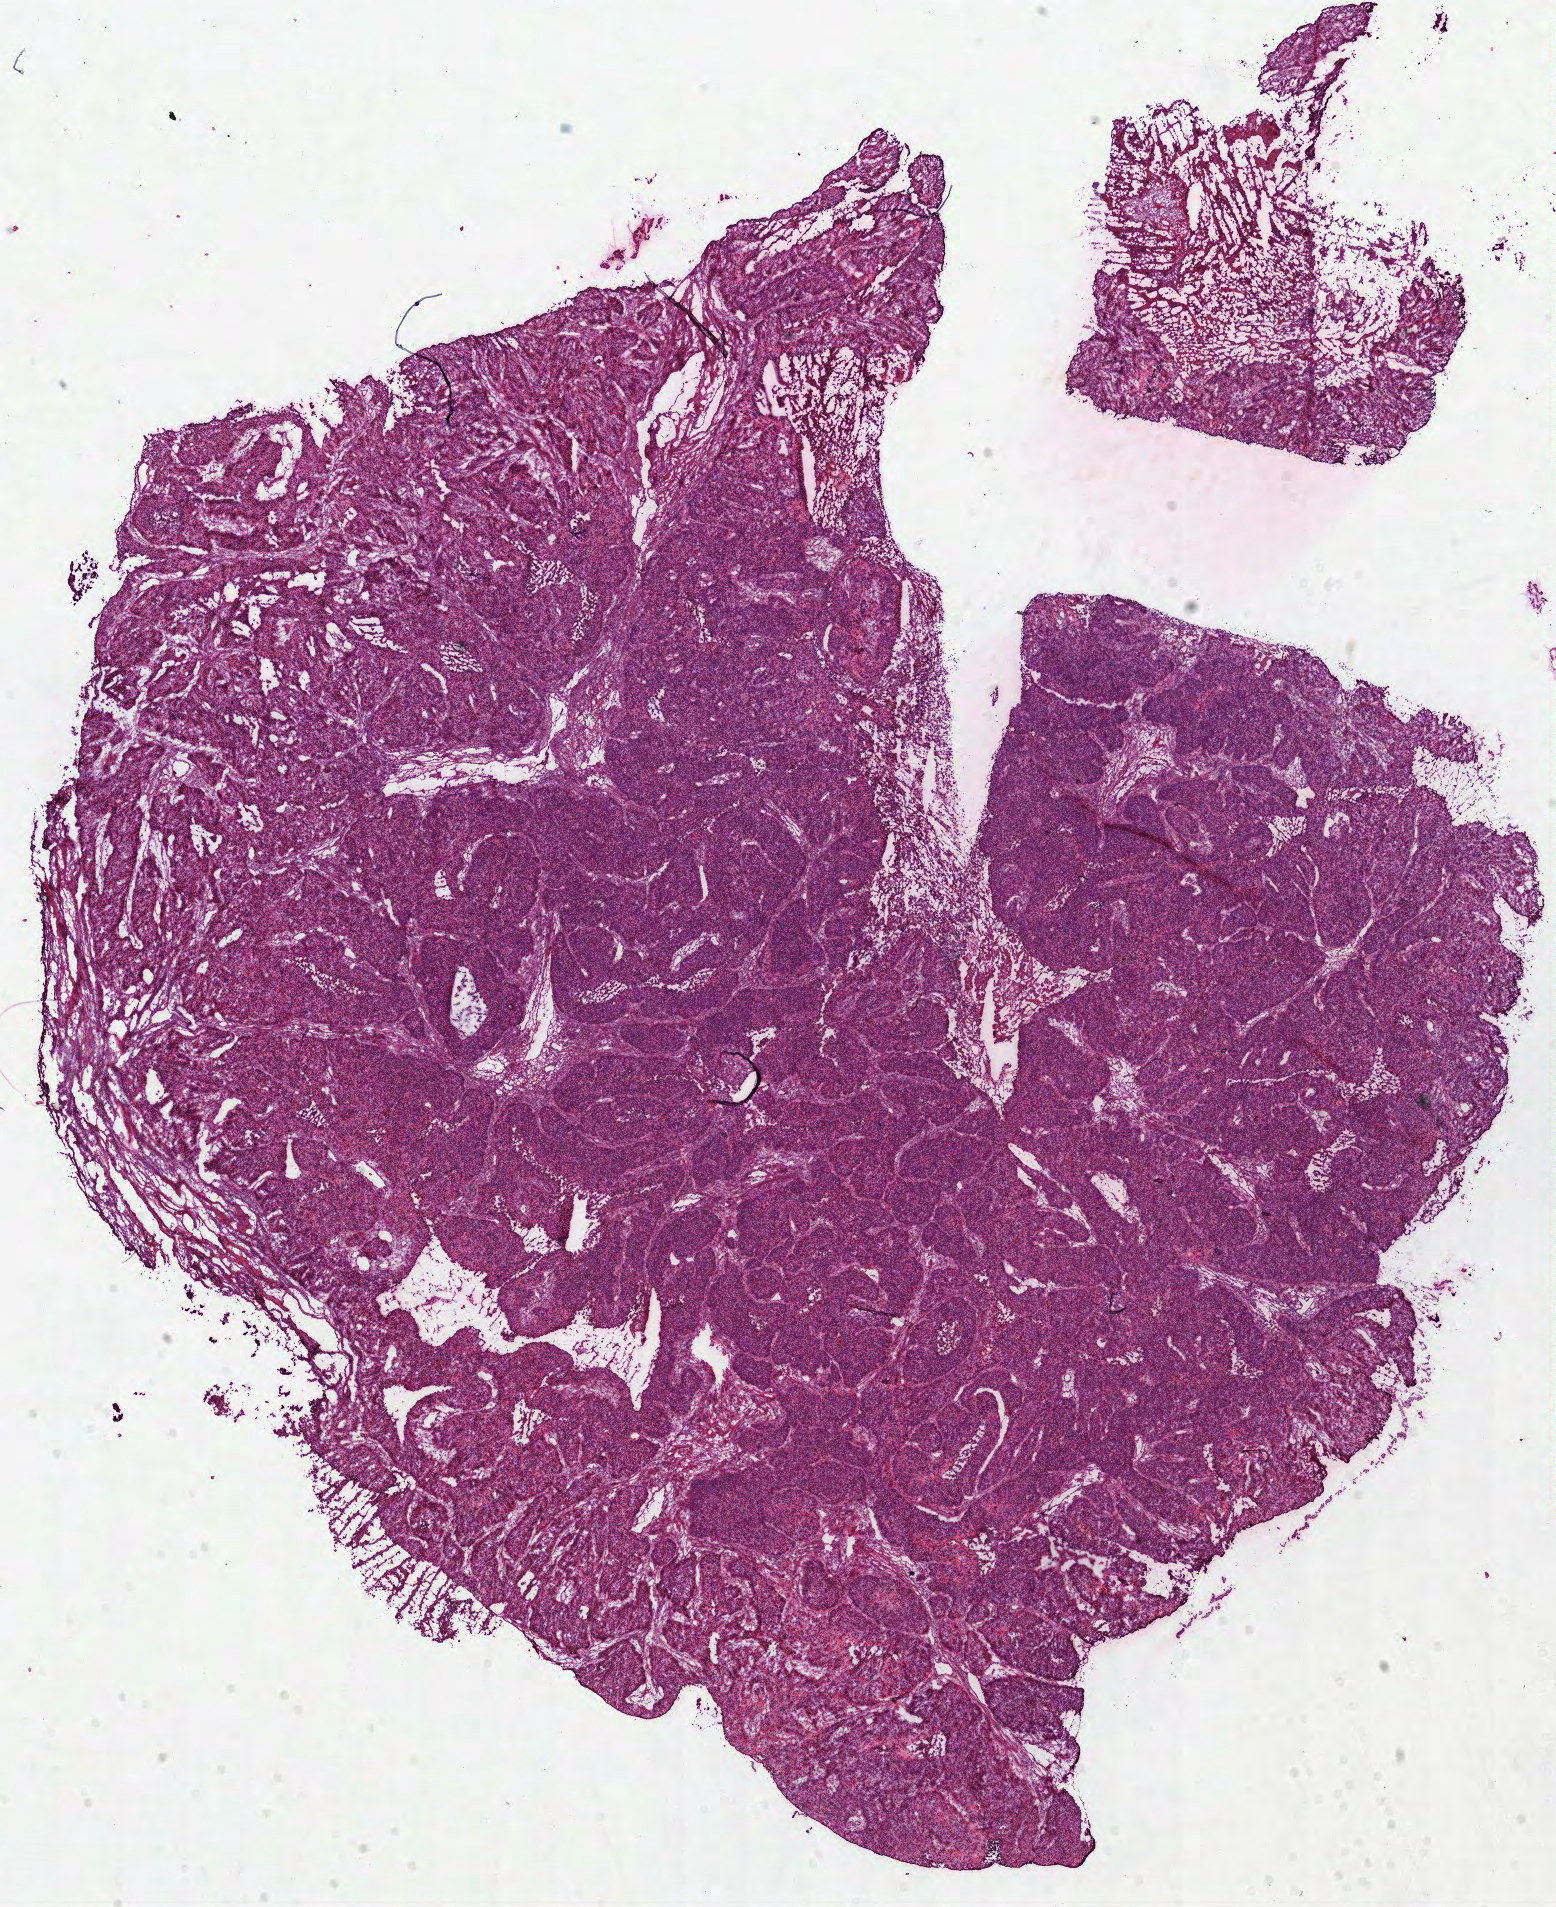
Whole-slide histology image, H&E — a low-resolution overview of the entire scanned area, about 12.2 x 15.0 mm; frozen section from the top of the tissue portion; sample: primary tumour, lung. Patient: male, age at initial diagnosis 65 years. Slide review estimates, as recorded: tumour cells 80%, tumour nuclei 85%, normal cells 0%, stromal cells 10%, necrosis 10%.
- laterality: right
- AJCC pathologic stage: IIA
- pathologic diagnosis: Papillary squamous cell carcinoma (upper lobe, lung)
- TNM: T3 N0 M0